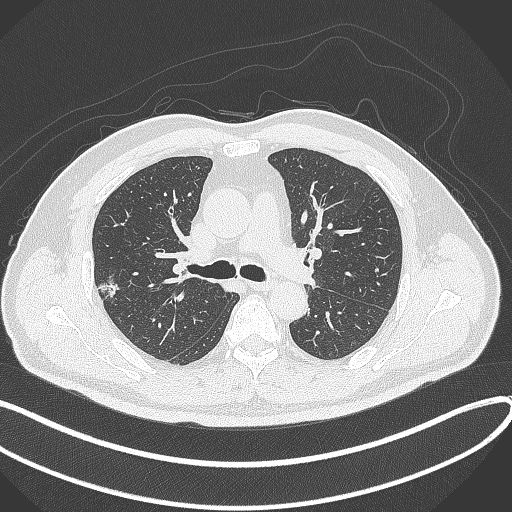
Chest CT, one axial slice. Slice 216 of 372 in the series (ordered by position). 120 kVp. Lung window (W 1500 / L -600 HU). 1 mm slice thickness. 512 × 512 image matrix, field of view 400 × 400 mm. Patient: male, 60 years. Case-level facts recorded for this patient, not image findings: clinical TNM (as recorded): T1c N0 M0.
Outlined on this slice (bounding box drawn by a radiologist):
- lung tumour (recorded histology: adenocarcinoma): bounding box (x1, y1, x2, y2) in pixels: (97, 273, 123, 302)